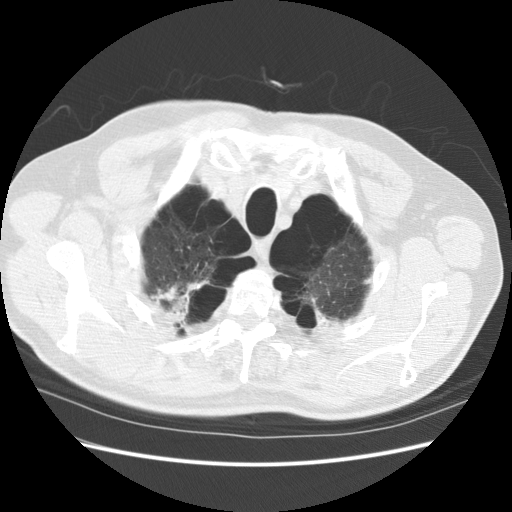
Axial slice from a low-dose chest CT screening exam; baseline screening round; lung window (W 1500 / L -600 HU); 2.5 mm slice thickness; standard (soft-tissue) reconstruction kernel (STANDARD); 120 kVp; slice 22 of 151 in the series; 512 × 512 image matrix. Male participant, aged 68 years at enrolment.
Lesion marked by an expert reader, bounding box (x1, y1, x2, y2) in pixels: (134, 266, 218, 331). The screening reader recorded 2 non-calcified nodules or masses ≥4 mm on this exam (left lower lobe, lingula); which of them this box marks is not recorded. Official screen result: positive, change unspecified: nodule(s) >= 4 mm or enlarging nodule(s), mass(es), or other non-specific abnormalities suspicious for lung cancer. Participant outcome: lung cancer diagnosed 1003 days after this screen — large cell carcinoma, NOS, right upper lobe, poorly differentiated (G3), stage IV (AJCC 6th edition).